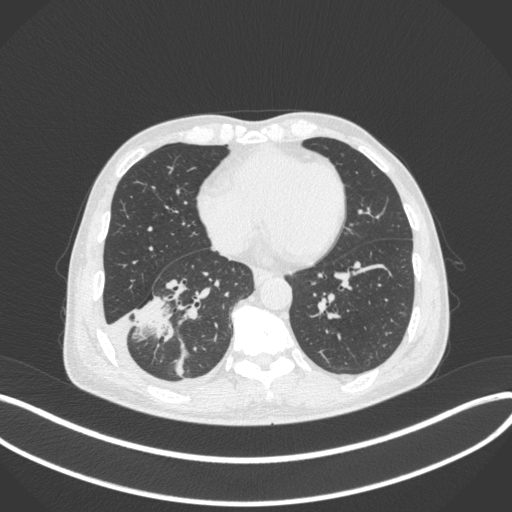
Chest CT, one axial slice; position 139 of 385 along the scan axis; lung window (W 1500 / L -600 HU); 512 × 512 image matrix, field of view 400 × 400 mm. Male patient, age 64 years. Case-level facts recorded for this patient, not image findings: clinical TNM (as recorded): T3 N0 M0; histopathological grade: G2-3.
Structures marked on this image (rectangle marked by the reading radiologist):
- lung tumour (recorded histology: adenocarcinoma): bounding box <126,289,176,346> (left, top, right, bottom; pixels)